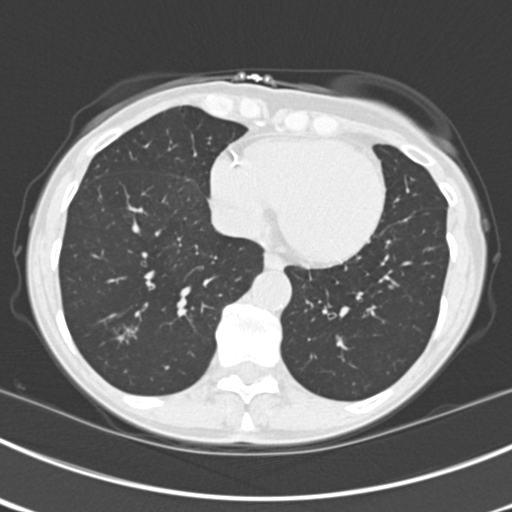
Axial slice from a low-dose chest CT screening exam; third annual screen; lung window (W 1500 / L -600 HU). Female participant, aged 63 years at enrolment. Current smoker at enrolment.
Lesion marked by an expert reader, bounding box (x1, y1, x2, y2) in pixels: (104, 311, 149, 358). The screening reader recorded 9 non-calcified nodules or masses ≥4 mm on this exam (left upper lobe, right upper lobe, left upper lobe, left lower lobe, right middle lobe, left lower lobe, left lower lobe, right lower lobe, right lower lobe); which of them this box marks is not recorded. Official screen result: positive, other. Participant outcome: lung cancer diagnosed 15 days after this screen — bronchiolo-alveolar adenocarcinoma, NOS, right upper lobe, right middle lobe, right lower lobe, left upper lobe, left lower lobe, moderately differentiated (G2), stage IV (AJCC 6th edition).